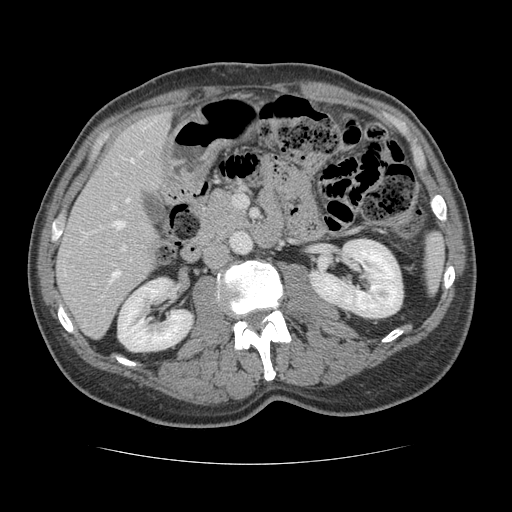
Contrast-enhanced abdominal CT, one axial slice. Position 58 of 134 along the scan axis. Reconstruction kernel STANDARD. 120 kVp. Intravenous contrast given. Soft-tissue window (W 400 / L 40 HU). 512 × 512 image matrix, field of view 377 × 377 mm. Male patient, age 68 years. Case-level facts recorded for this patient, not image findings: diagnosis: colorectal cancer liver metastases, imaged before liver resection; multiple liver metastases: yes; largest metastasis: 2.2 cm; disease in both lobes: no.
Structures marked on this image (expert manual segmentation):
- hepatic veins: bounding box (x1, y1, x2, y2) in pixels: (113, 152, 141, 229)
- liver: (58, 113, 171, 336)
- planned liver remnant (the part of the liver to remain after resection): (58, 113, 171, 335)
- portal vein (with intrahepatic branches): (109, 206, 125, 283)